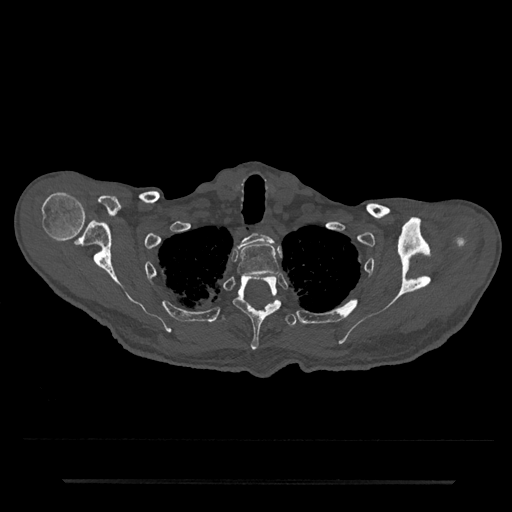
CT including the spine, one axial slice. Slice 665 of 797 in the series (ordered by position). Reconstruction kernel Br40s/3. 120 kVp. Bone window (W 1800 / L 400 HU). 512 × 512 image matrix. Male patient, age 74 years. From the clinical record (not read from this slice): primary cancer: prostate.
Outlined on this slice (semi-automatically segmented with operator editing):
- T1 vertebra: box from (x=238, y=233) to (x=274, y=248) px
- T2 vertebra: (x=237, y=244)–(x=280, y=276)
- T3 vertebra: (x=233, y=275)–(x=282, y=351)
- T4 vertebra: (x=220, y=314)–(x=297, y=328)